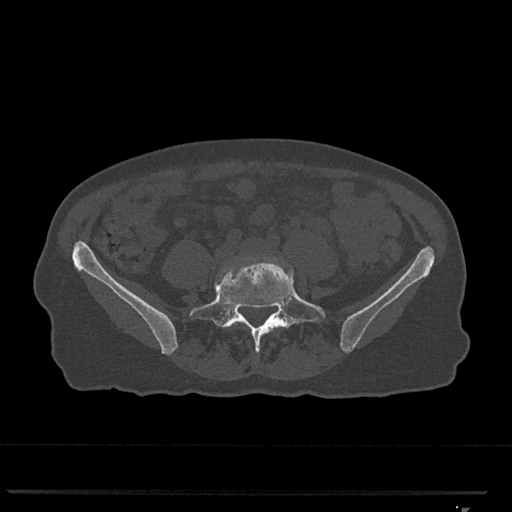
CT including the spine, one axial slice; slice 163 of 793 in the series (ordered by position); 120 kVp; bone window (W 1800 / L 400 HU); 0.5 mm slice thickness; 512 × 512 image matrix, field of view 380 × 380 mm. Patient: female, 62 years. From the clinical record (not read from this slice): primary cancer: renal.
Structures marked on this image (semi-automatic segmentation, software-assisted and operator-edited):
- L4 vertebra: bounding box [x1, y1, x2, y2] px = [218, 258, 257, 325]
- L5 vertebra: [189, 258, 326, 353]